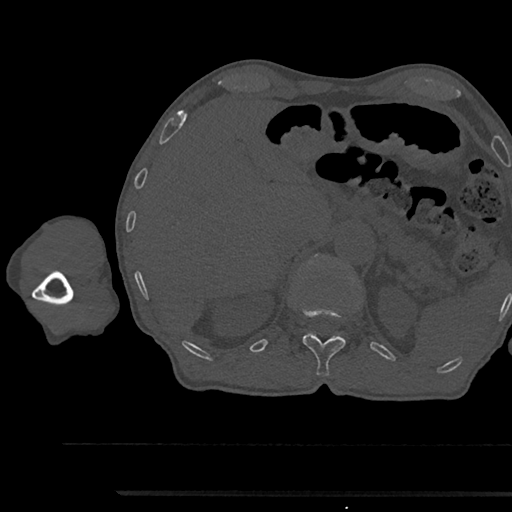
CT including the spine, one axial slice. Position 693 of 797 along the scan axis. Bone window (W 1800 / L 400 HU). 0.5 mm slice thickness. 512 × 512 image matrix, field of view 367 × 367 mm. Patient: male, 79 years. Case-level facts recorded for this patient, not image findings: primary cancer: prostate.
Outlined on this slice (semi-automatically segmented with operator editing):
- T12 vertebra: box from (x=302, y=310) to (x=346, y=376) px